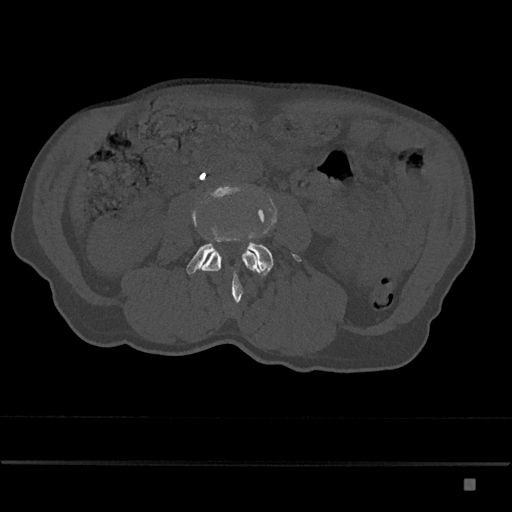
CT including the spine, one axial slice. Position 372 of 797 along the scan axis. Reconstruction kernel Br40s/3. 120 kVp. Bone window (W 1800 / L 400 HU). 512 × 512 image matrix, field of view 390 × 390 mm. Male patient, age 72 years. From the clinical record (not read from this slice): primary cancer: prostate.
Structures marked on this image (semi-automatically segmented with operator editing):
- L3 vertebra: box from (x=192, y=184) to (x=260, y=304) px
- L4 vertebra: (x=186, y=241)–(x=302, y=277)